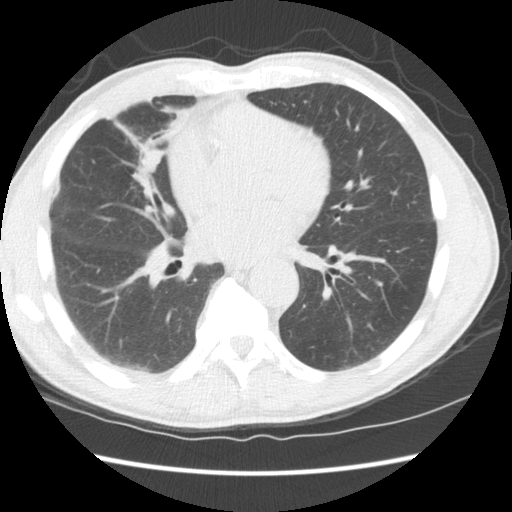
Low-dose screening chest CT, one axial slice; slice 66 of 147 in the series (ordered by position); lung window (W 1500 / L -600 HU); 2.5 mm slice thickness; 512 × 512 image matrix.
Structures marked on this image (expert manual segmentation):
- lesion 1 (tumor, middle lobe of right lung): box from (x=142, y=147) to (x=163, y=171) px